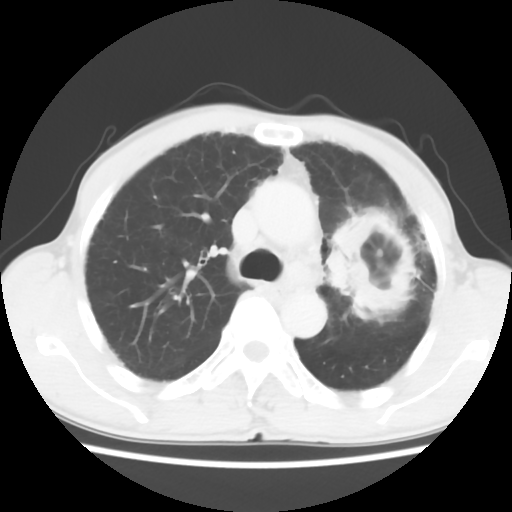
Chest CT, one axial slice. Slice 41 of 60 in the series (ordered by position). Reconstruction kernel STANDARD. 120 kVp. Lung window (W 1500 / L -600 HU). 512 × 512 image matrix. Patient: male, 64 years. Case-level facts recorded for this patient, not image findings: clinical TNM (as recorded): T3 N3 M0; histopathological grade: G3.
Structures marked on this image (bounding box drawn by a radiologist):
- lung tumour (recorded histology: adenocarcinoma): box from (x=322, y=199) to (x=428, y=333) px